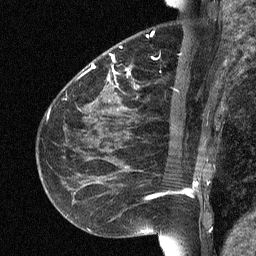
Breast MRI (dynamic contrast-enhanced), one sagittal slice; dynamic contrast-enhanced study with each time point stored as its own series, time point 2 of 3 at this slice position (early post-contrast, ordered by acquisition time); 1.5 T; TE 4.8 ms, TR 27 ms; 2 mm slice thickness; 256 × 256 image matrix. Patient: female, 51 years. Case-level facts recorded for this patient, not image findings: setting: breast cancer imaged before/during neoadjuvant chemotherapy; receptor status: HR-positive, HER2-negative.
Outlined on this slice (semi-automatically segmented with operator editing):
- analysis volume of interest (the breast-tissue region the enhancement analysis was run in; not a lesion): box from (x=72, y=34) to (x=182, y=118) px
- tumour enhancement mask (voxels above the 90 % enhancement threshold inside the analysis volume of interest): (x=92, y=65)–(x=95, y=68)